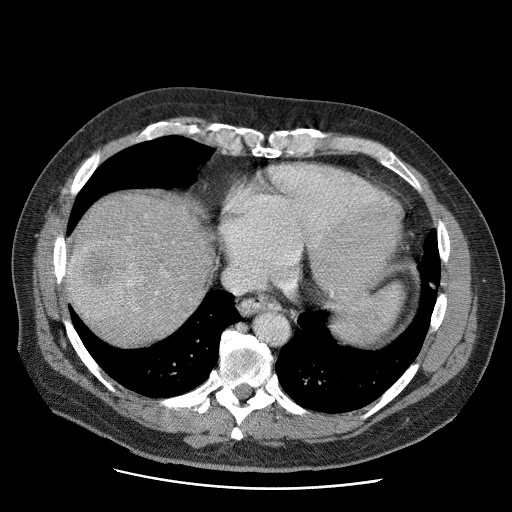
Contrast-enhanced abdominal CT (liver protocol), one axial slice; reconstruction kernel STANDARD; 120 kVp; soft-tissue window (W 400 / L 40 HU); 512 × 512 image matrix. Case-level facts recorded for this patient, not image findings: diagnosis: hepatocellular carcinoma (patient treated with transarterial chemoembolisation; whether this scan precedes or follows treatment is not stated here); TNM stage (as recorded): Stage-IIIA; Child-Pugh class: A; tumour differentiation: moderately differentiated; tumour nodularity: multinodular.
Structures marked on this image (semi-automatic segmentation, software-assisted and operator-edited):
- liver parenchyma outside the tumour (the mass and vessels are separate outlines, so this box may not span the whole liver): bounding box <64,192,212,342> (left, top, right, bottom; pixels)
- mass: <66,237,142,319>